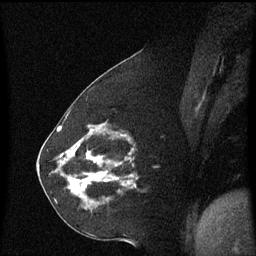
Breast MRI (dynamic contrast-enhanced), one sagittal slice; position 24 of 60 along the scan axis; dynamic contrast-enhanced series, image 2 of 3 at this slice position (ordered by acquisition); 1.5 T; TE 4.2 ms, TR 8.4 ms; 2.2 mm slice thickness; 256 × 256 image matrix, field of view 200 × 200 mm. Female patient, age 60 years. Case-level facts recorded for this patient, not image findings: setting: breast cancer imaged before/during neoadjuvant chemotherapy; receptor status: triple-negative.
Structures marked on this image (semi-automatic segmentation, software-assisted and operator-edited):
- analysis volume of interest (the breast-tissue region the enhancement analysis was run in; not a lesion): bounding box (x1, y1, x2, y2) in pixels: (68, 142, 136, 211)
- tumour enhancement mask (voxels above the 70 % enhancement threshold inside the analysis volume of interest): (70, 152, 120, 191)